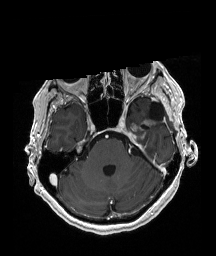
Brain MRI from a brain-tumour surgery series, one axial slice. Slice 136 of 192 in the series (ordered by position). T1-weighted post-contrast. 1 mm slice thickness. 216 × 256 image matrix, field of view 211 × 250 mm. Case-level facts recorded for this patient, not image findings: histopathology: Glioblastoma; WHO grade: 4; IDH mutation: no; tumour location: Left Temporal.
Outlined on this slice (manually delineated by an expert):
- previous resection cavity: bounding box <149,102,163,121> (left, top, right, bottom; pixels)